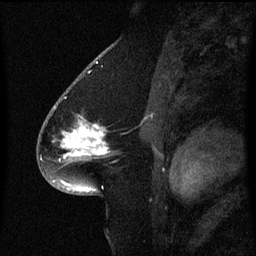
Breast MRI (dynamic contrast-enhanced), one sagittal slice. Slice 36 of 60 in the series (ordered by position). Dynamic contrast-enhanced series, image 2 of 3 at this slice position (ordered by acquisition). 1.5 T. TE 4.2 ms, TR 8.4 ms. 2 mm slice thickness. 256 × 256 image matrix, field of view 200 × 200 mm. Patient: female, 54 years. From the clinical record (not read from this slice): setting: breast cancer imaged before/during neoadjuvant chemotherapy; receptor status: HR-positive, HER2-negative.
Structures marked on this image (semi-automatic segmentation, software-assisted and operator-edited):
- analysis volume of interest (the breast-tissue region the enhancement analysis was run in; not a lesion): bounding box (x1, y1, x2, y2) in pixels: (46, 100, 111, 169)
- tumour enhancement mask (voxels above the 70 % enhancement threshold inside the analysis volume of interest): (63, 124, 108, 157)